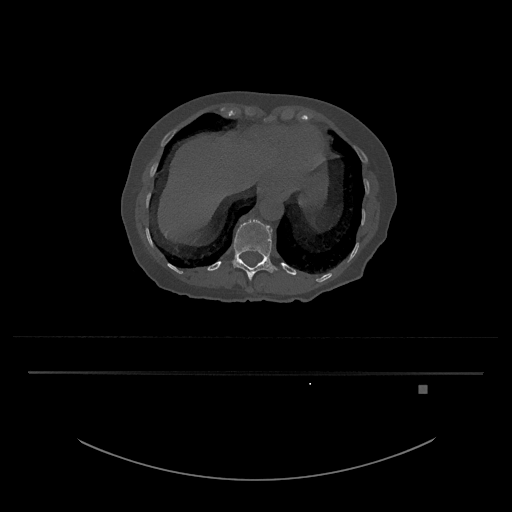
CT including the spine, one axial slice. Slice 612 of 797 in the series (ordered by position). Bone window (W 1800 / L 400 HU). 512 × 512 image matrix, field of view 500 × 500 mm. Female patient, age 57 years. Case-level facts recorded for this patient, not image findings: primary cancer: cervical.
Annotated regions visible in this slice (semi-automatically segmented with operator editing):
- T12 vertebra: bounding box (x1, y1, x2, y2) in pixels: (232, 219, 278, 281)